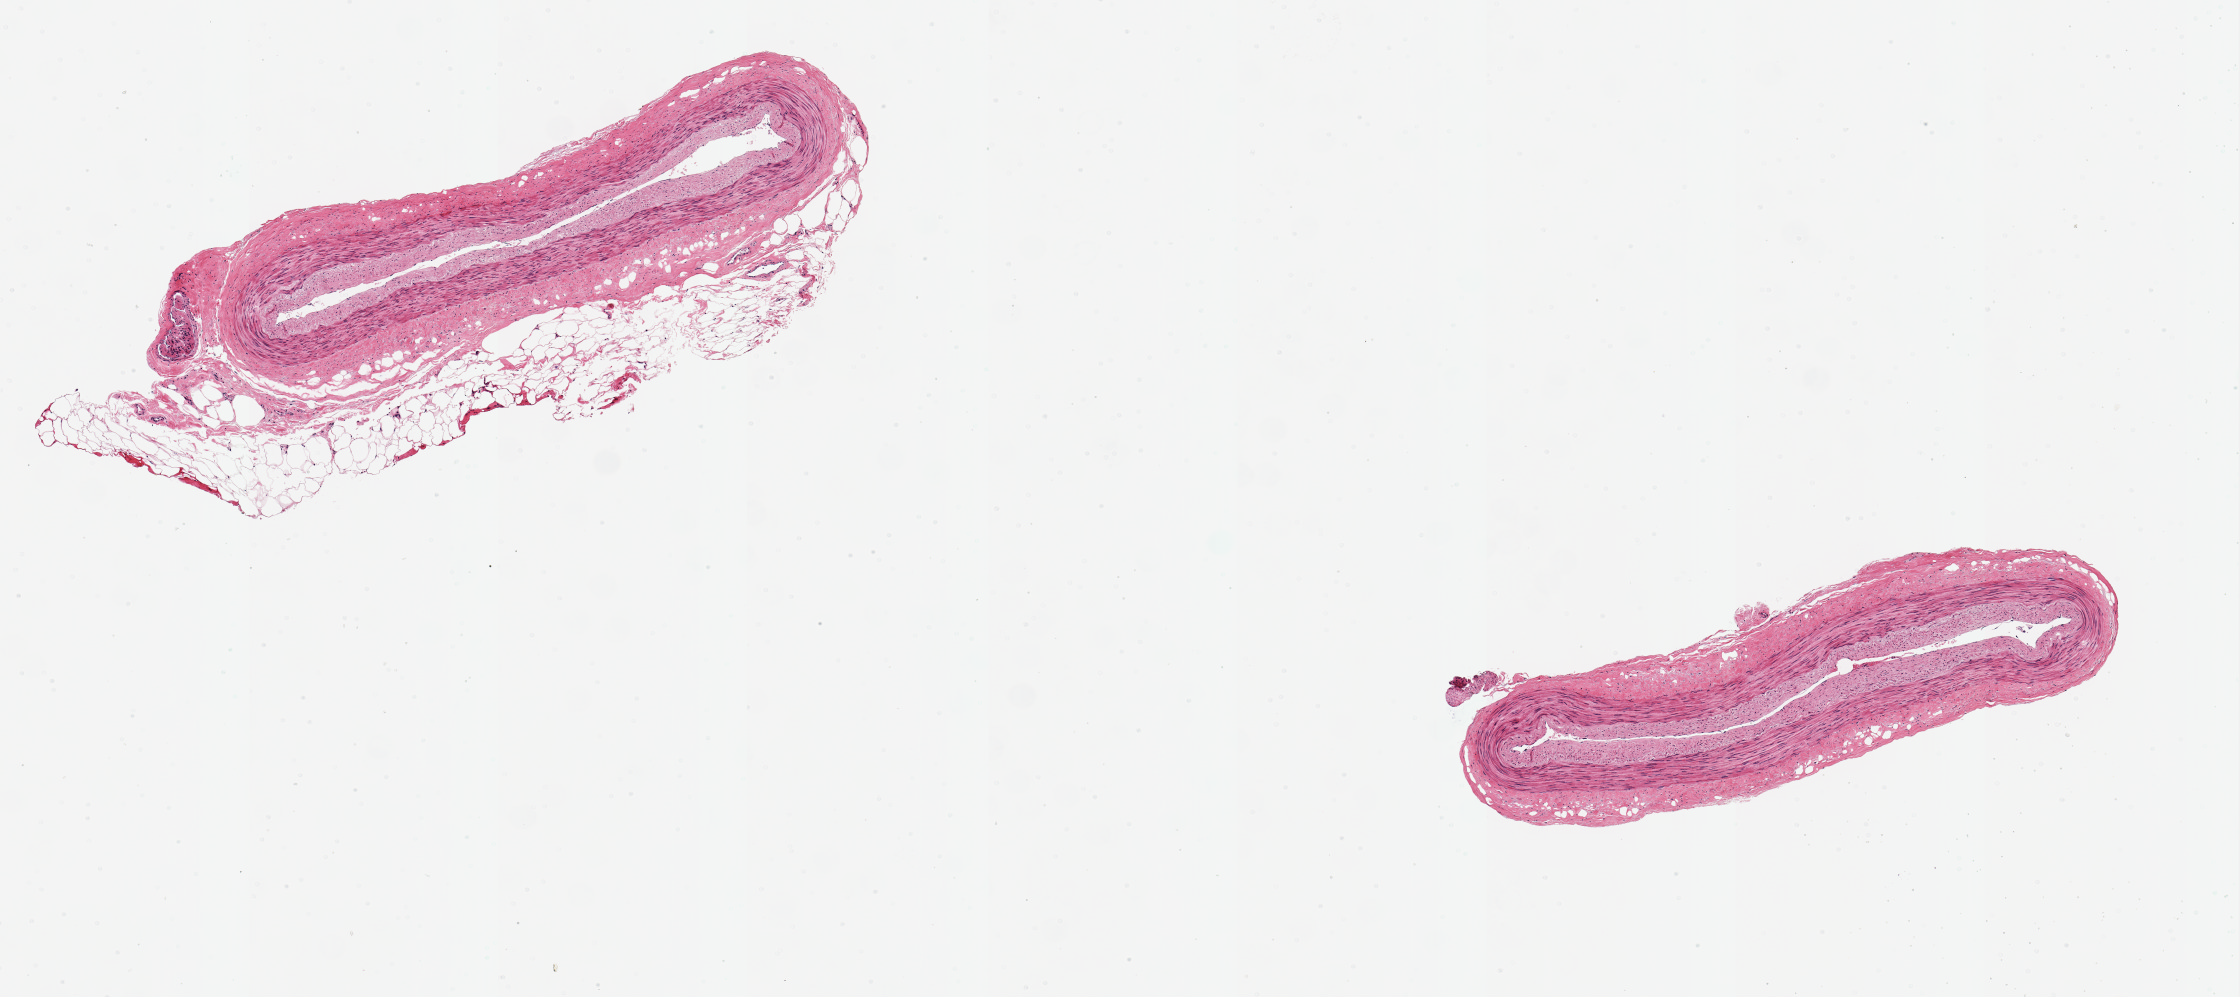
Whole-slide image, haematoxylin and eosin stain — shown as a low-resolution overview of the whole scanned area (about 8.9 x 3.9 mm, slide scanned at 20x), PAXgene-fixed paraffin-embedded (PFPE) section, section of tibial artery (target tissue), tissue donor sample. Donor: female.
Reviewer comment on this tissue sample: 2 aliquots, ~2.4x0.5mm, one with small amount adherent fat, other good clean specimen.